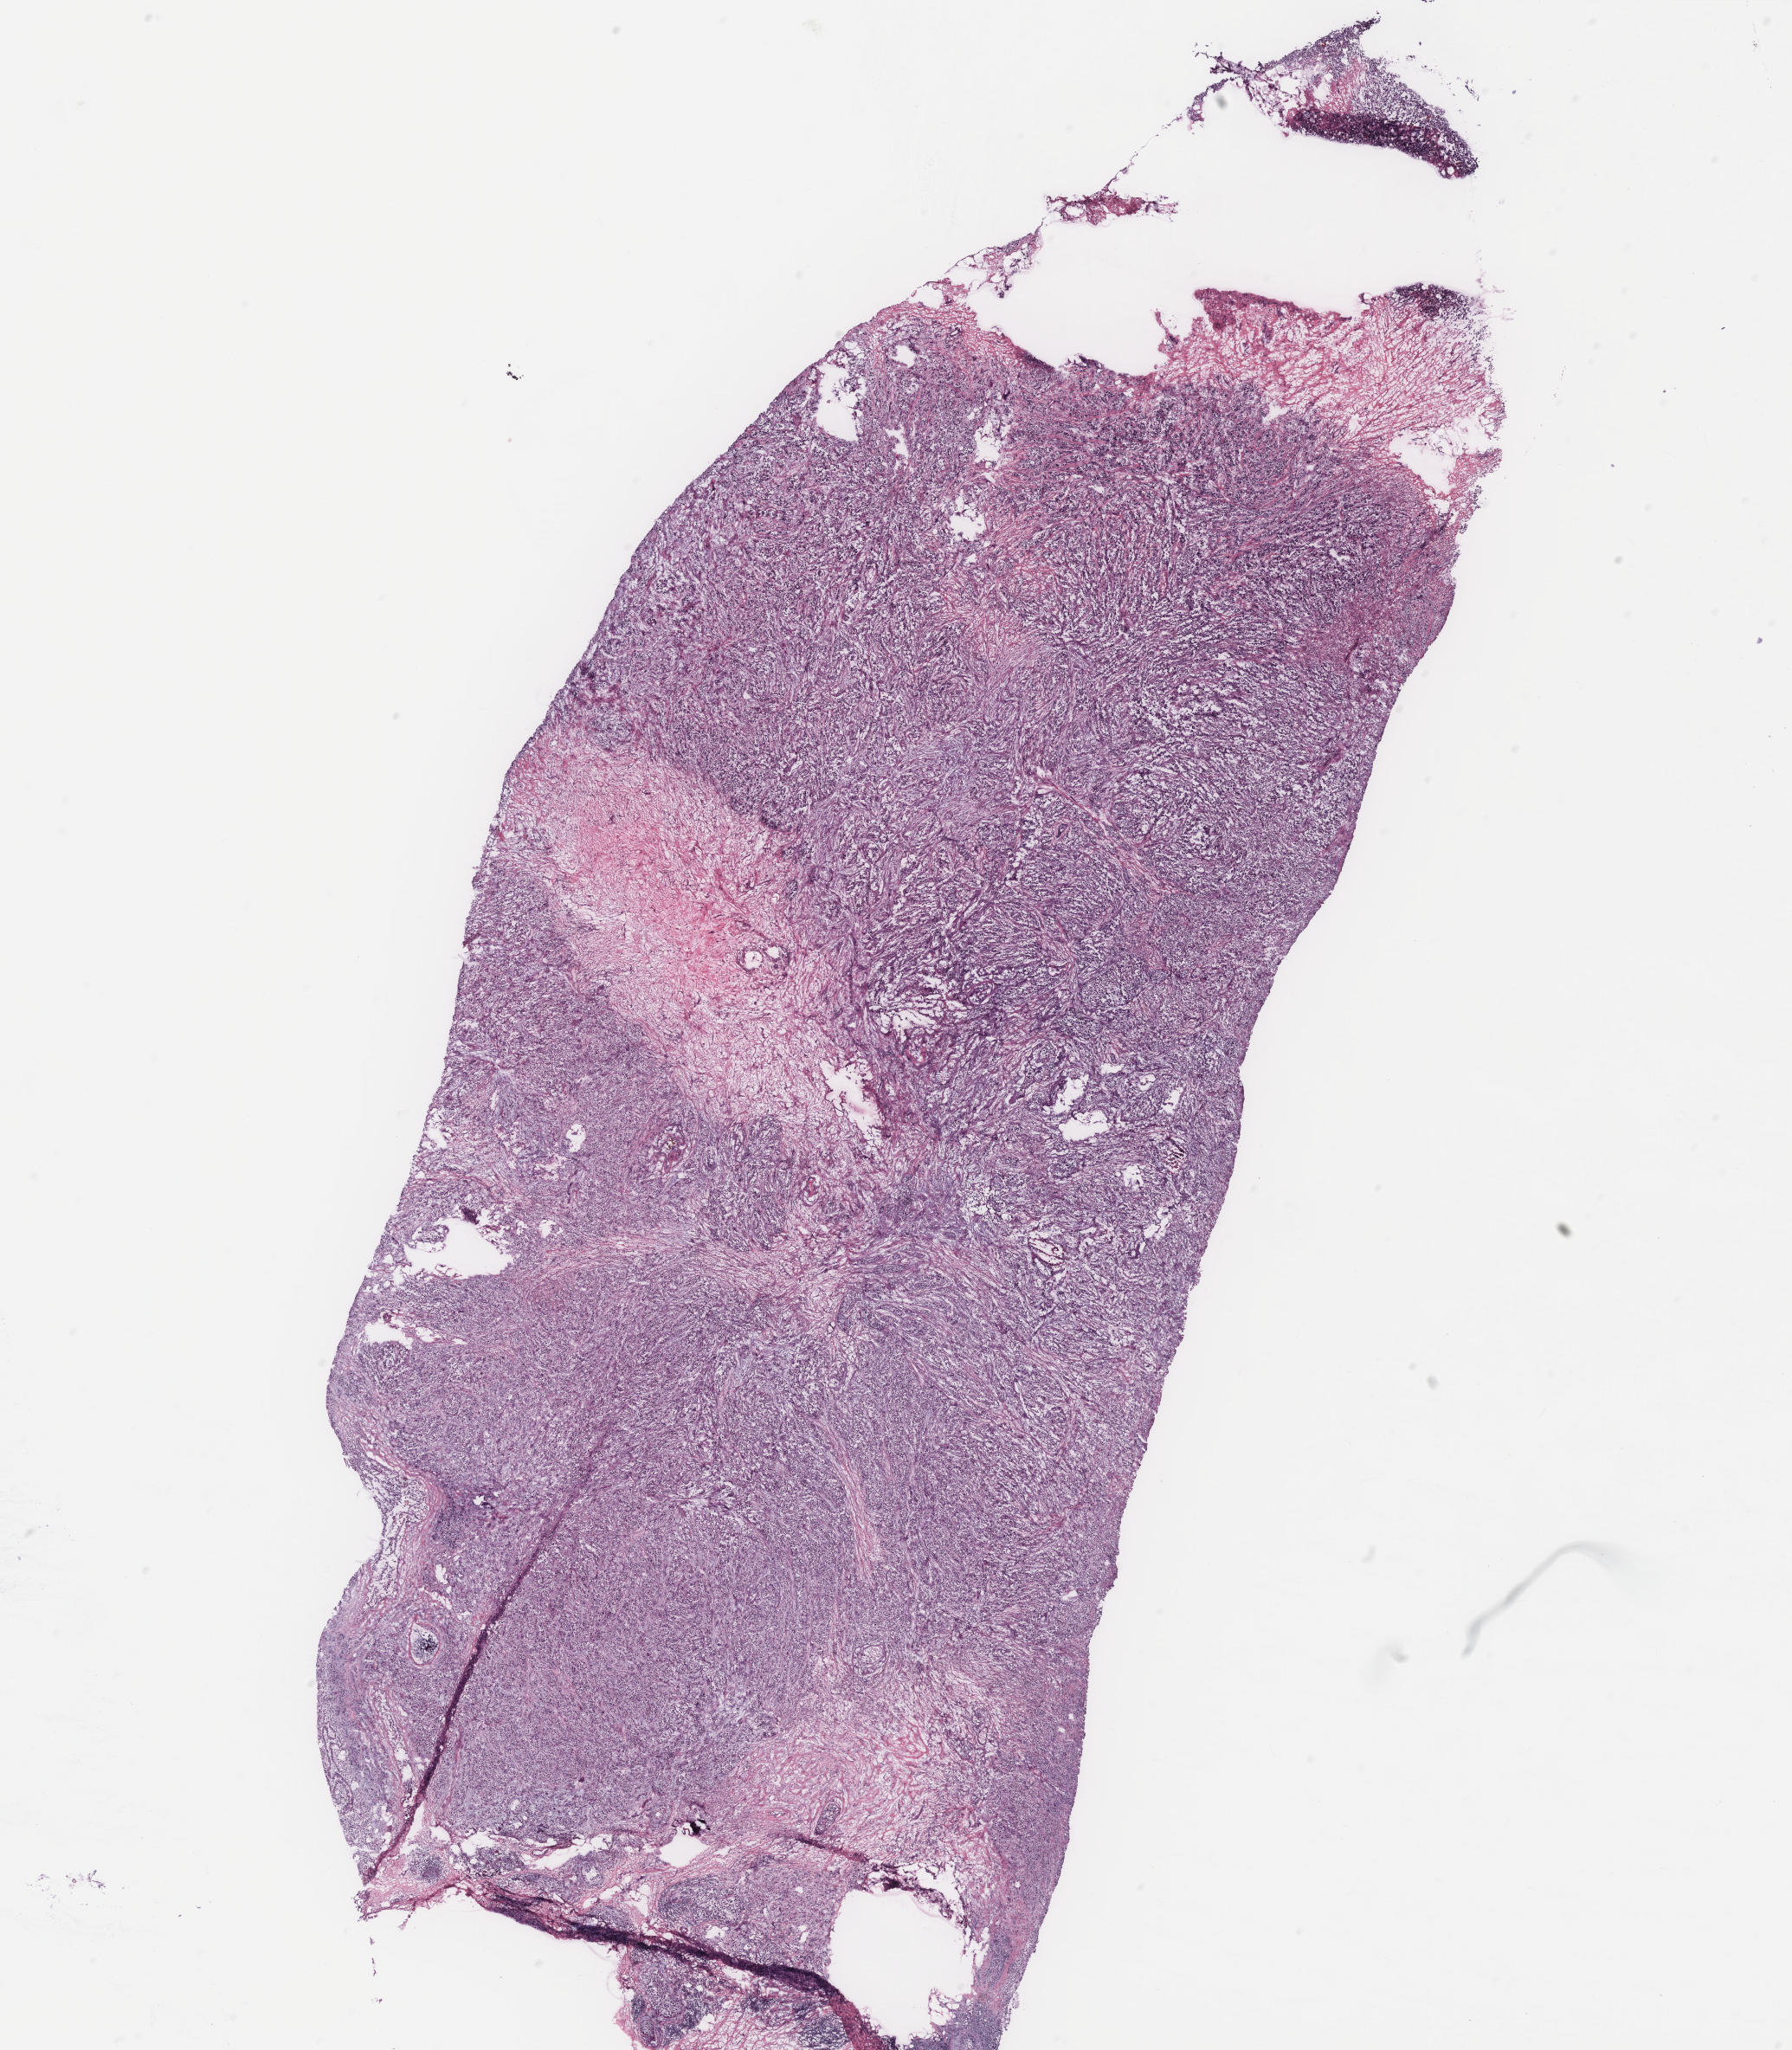
H&E-stained whole-slide image — whole scanned area (about 16.6 x 19.0 mm, slide scanned at 40x) shown as a low-resolution overview, tumour tissue sample, breast. Patient: female, age 75 years.
Histologic diagnosis: Infiltrating duct carcinoma, NOS. AJCC pathologic stage: IIA.